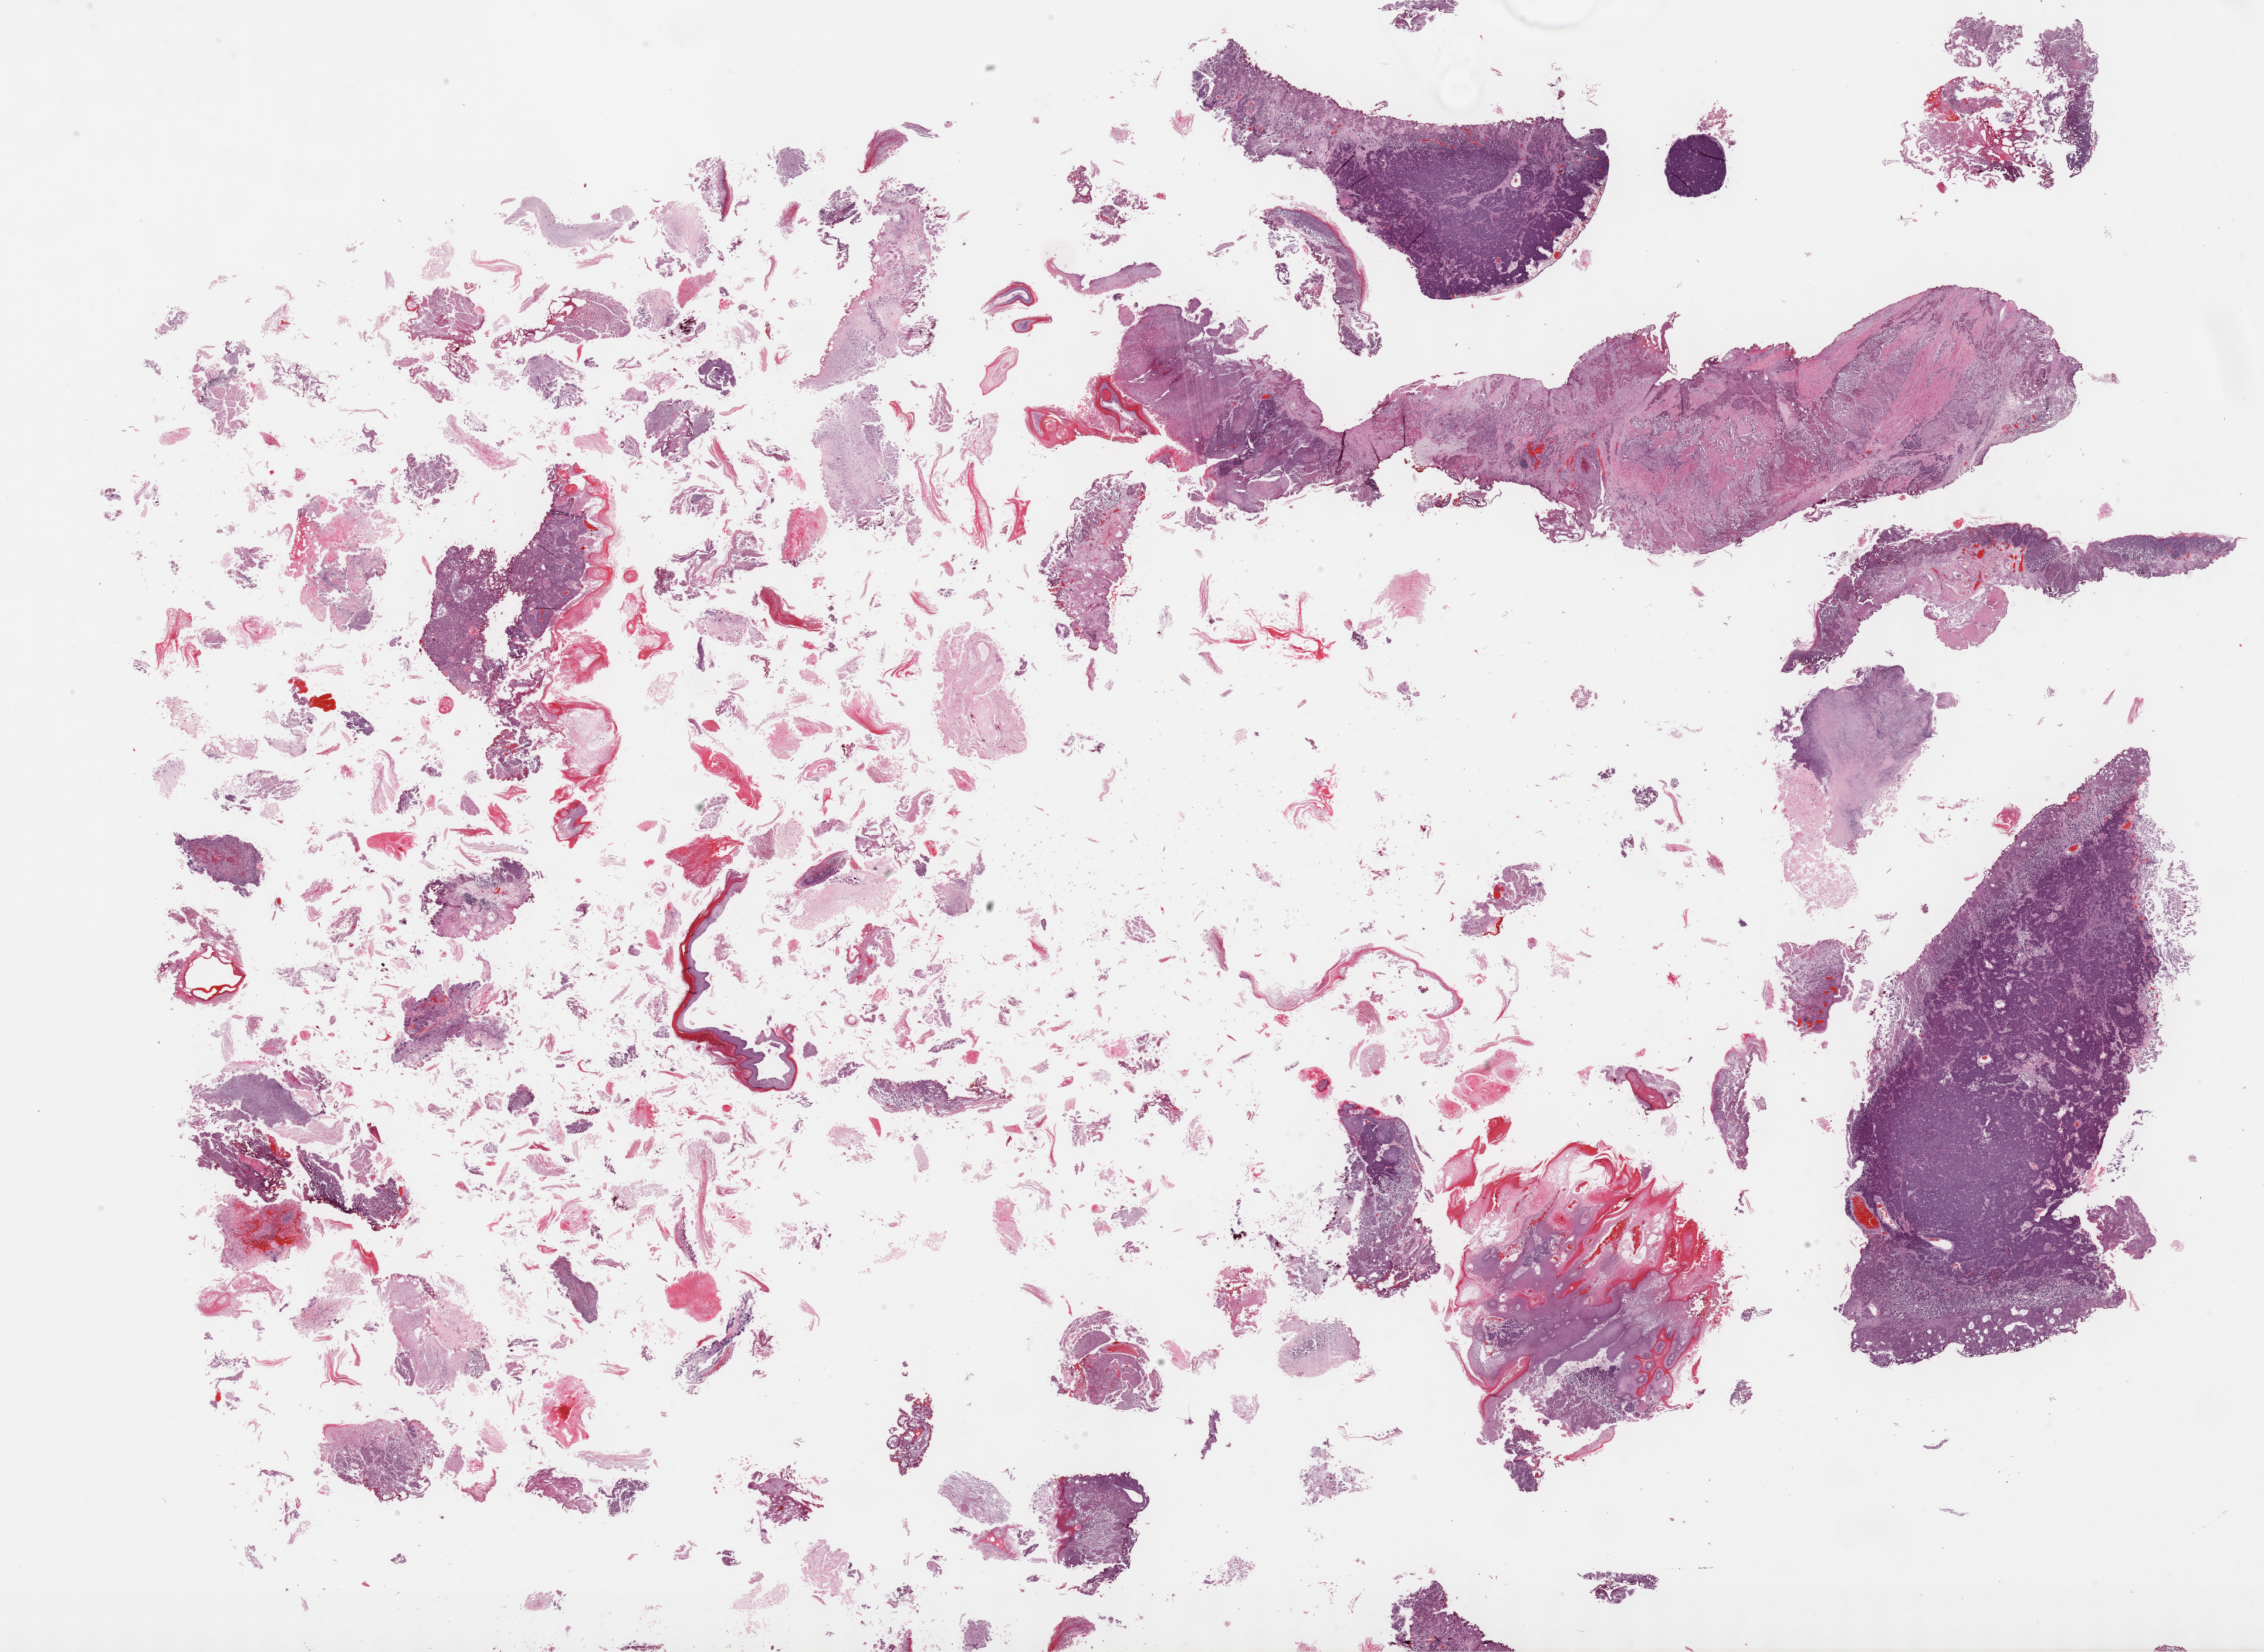
Digitized Hematoxylin and eosin (H&E) stained tissue section (whole slide), whole scanned area (about 31.2 x 22.8 mm, from a 40x scan) shown as a low-resolution overview; formalin-fixed paraffin-embedded (FFPE) diagnostic section; sample: primary tumour, bladder. Male, age 71 years at initial diagnosis. Histologic grade: high grade.
AJCC pathologic stage: IV (7th edition). Pathologic diagnosis: Transitional cell carcinoma.